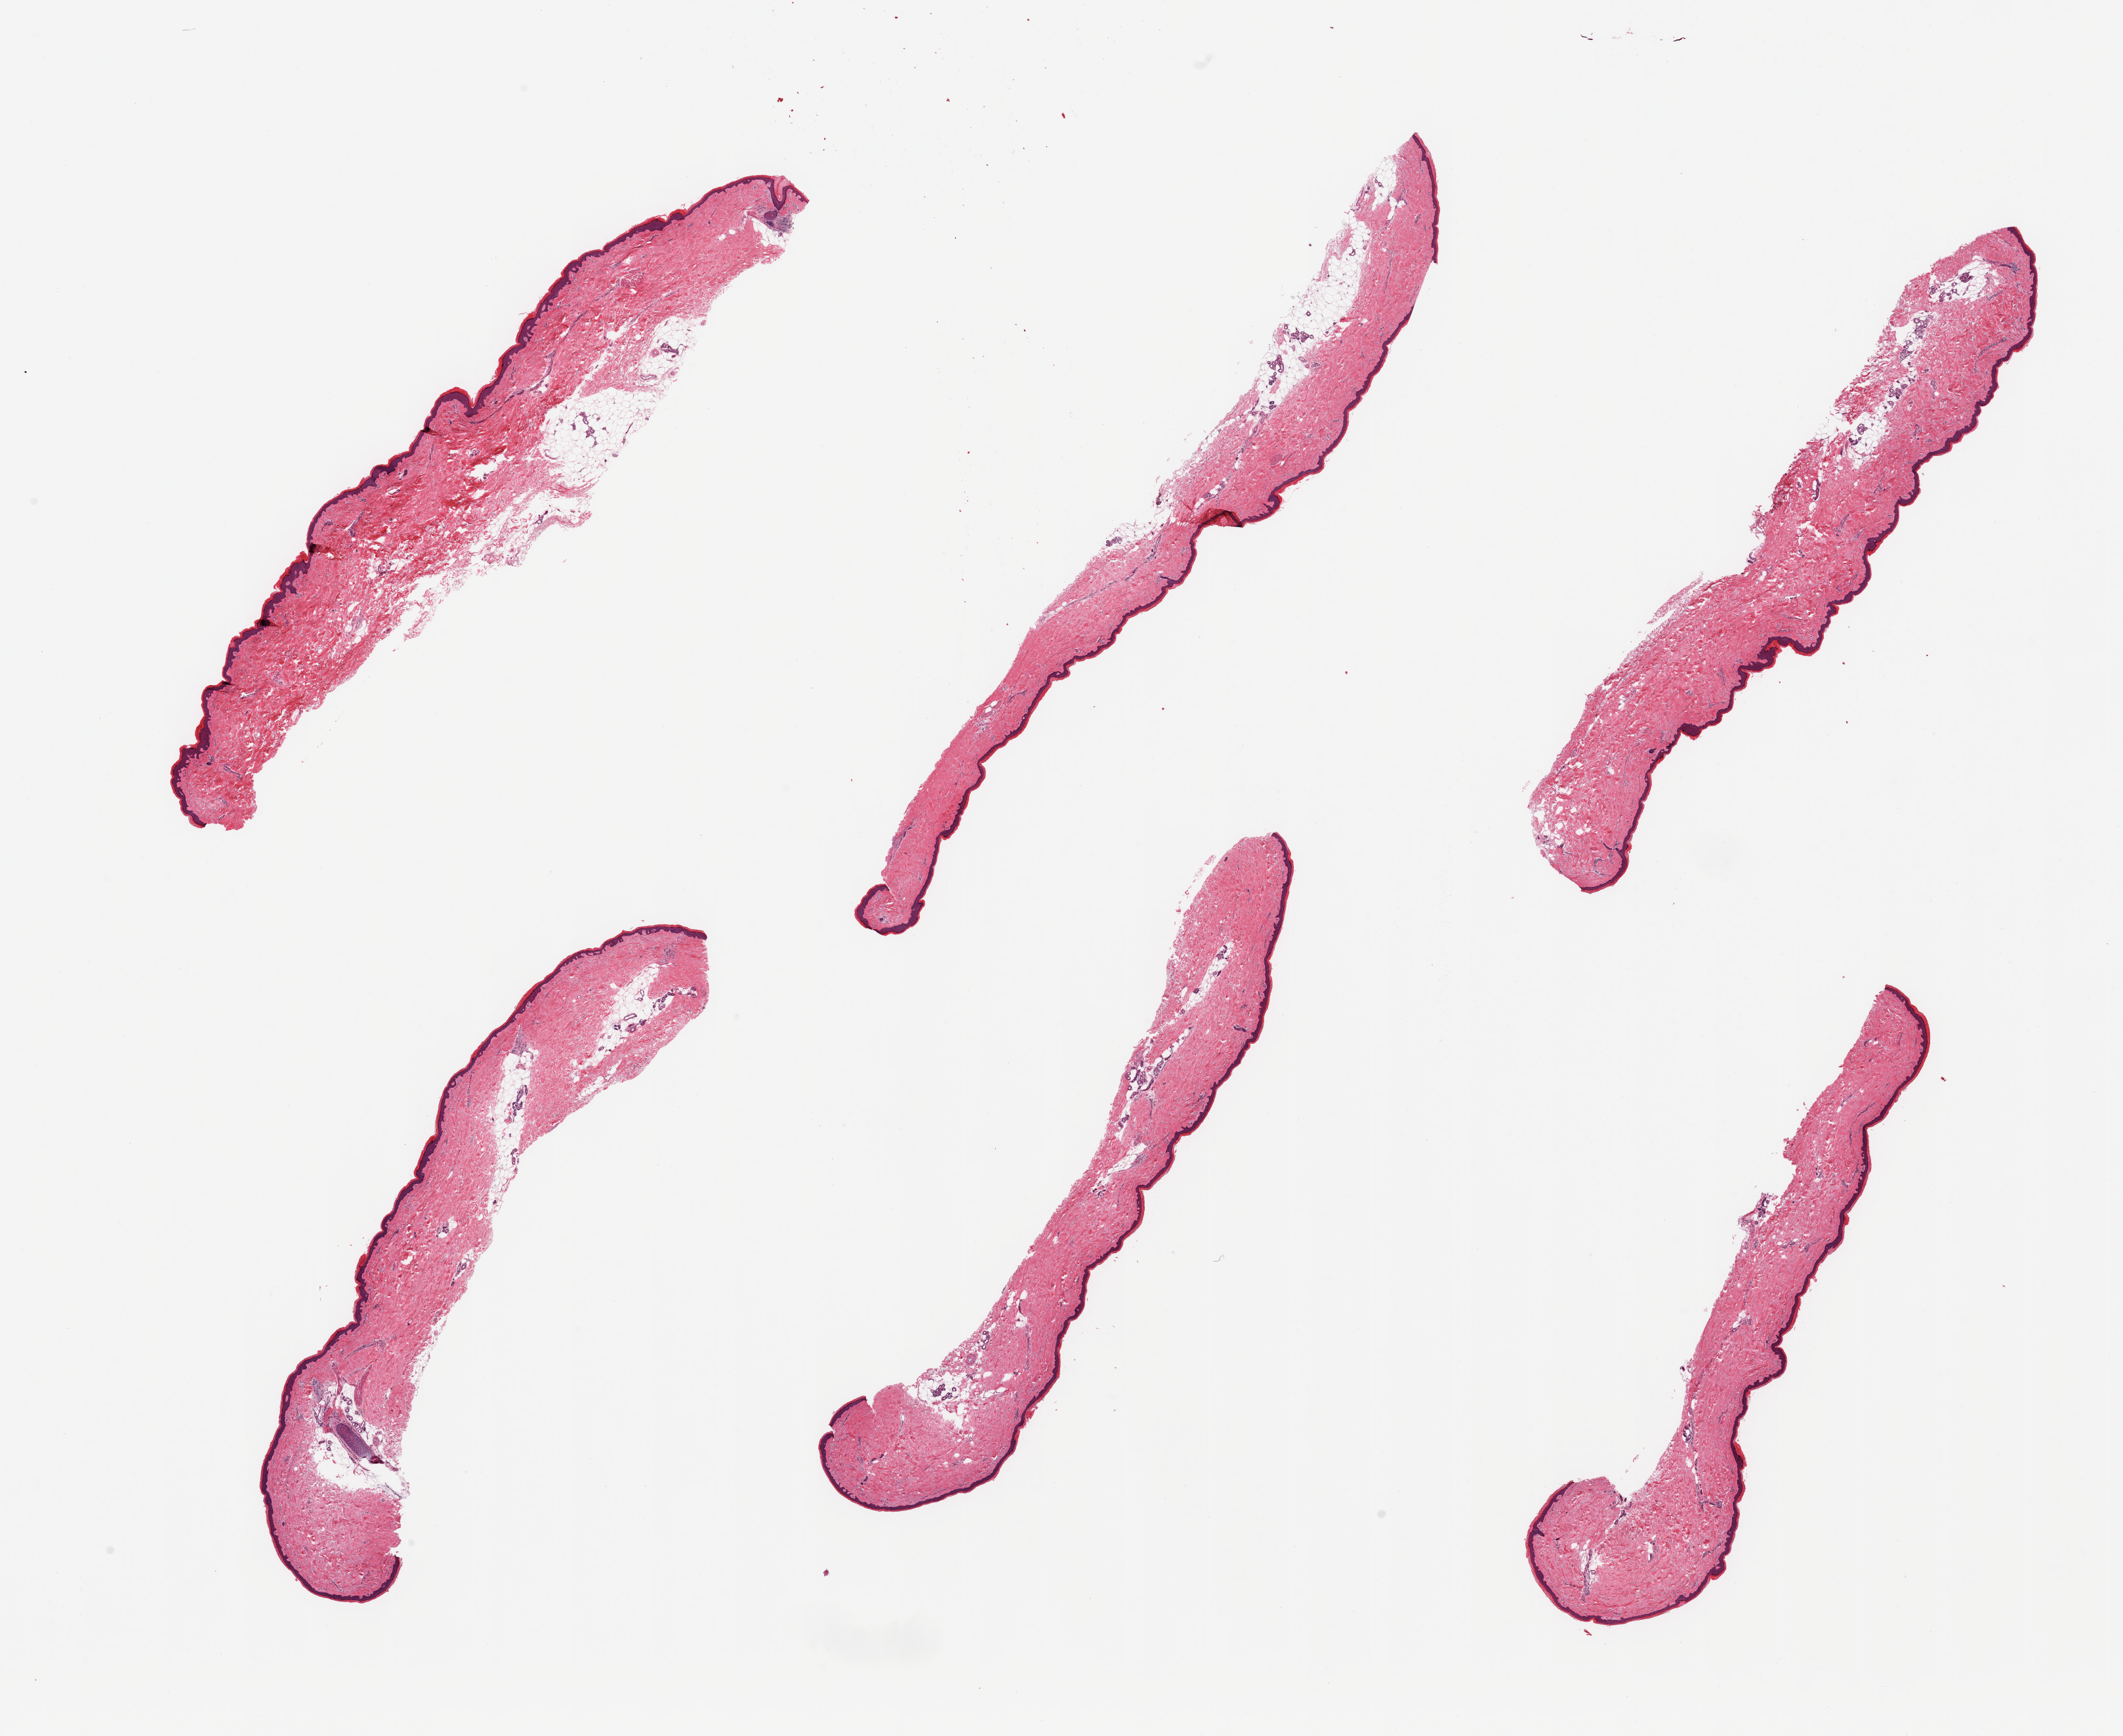
Digitized H&E-stained section, whole scanned area (about 25.6 x 20.9 mm) shown as a low-resolution overview, PAXgene-fixed, paraffin-embedded tissue, section of skin of lower leg (target tissue), donor tissue sample.
* pathologist's review note for this sample: 6 pieces; generally well trimmed; 10% dermal fat